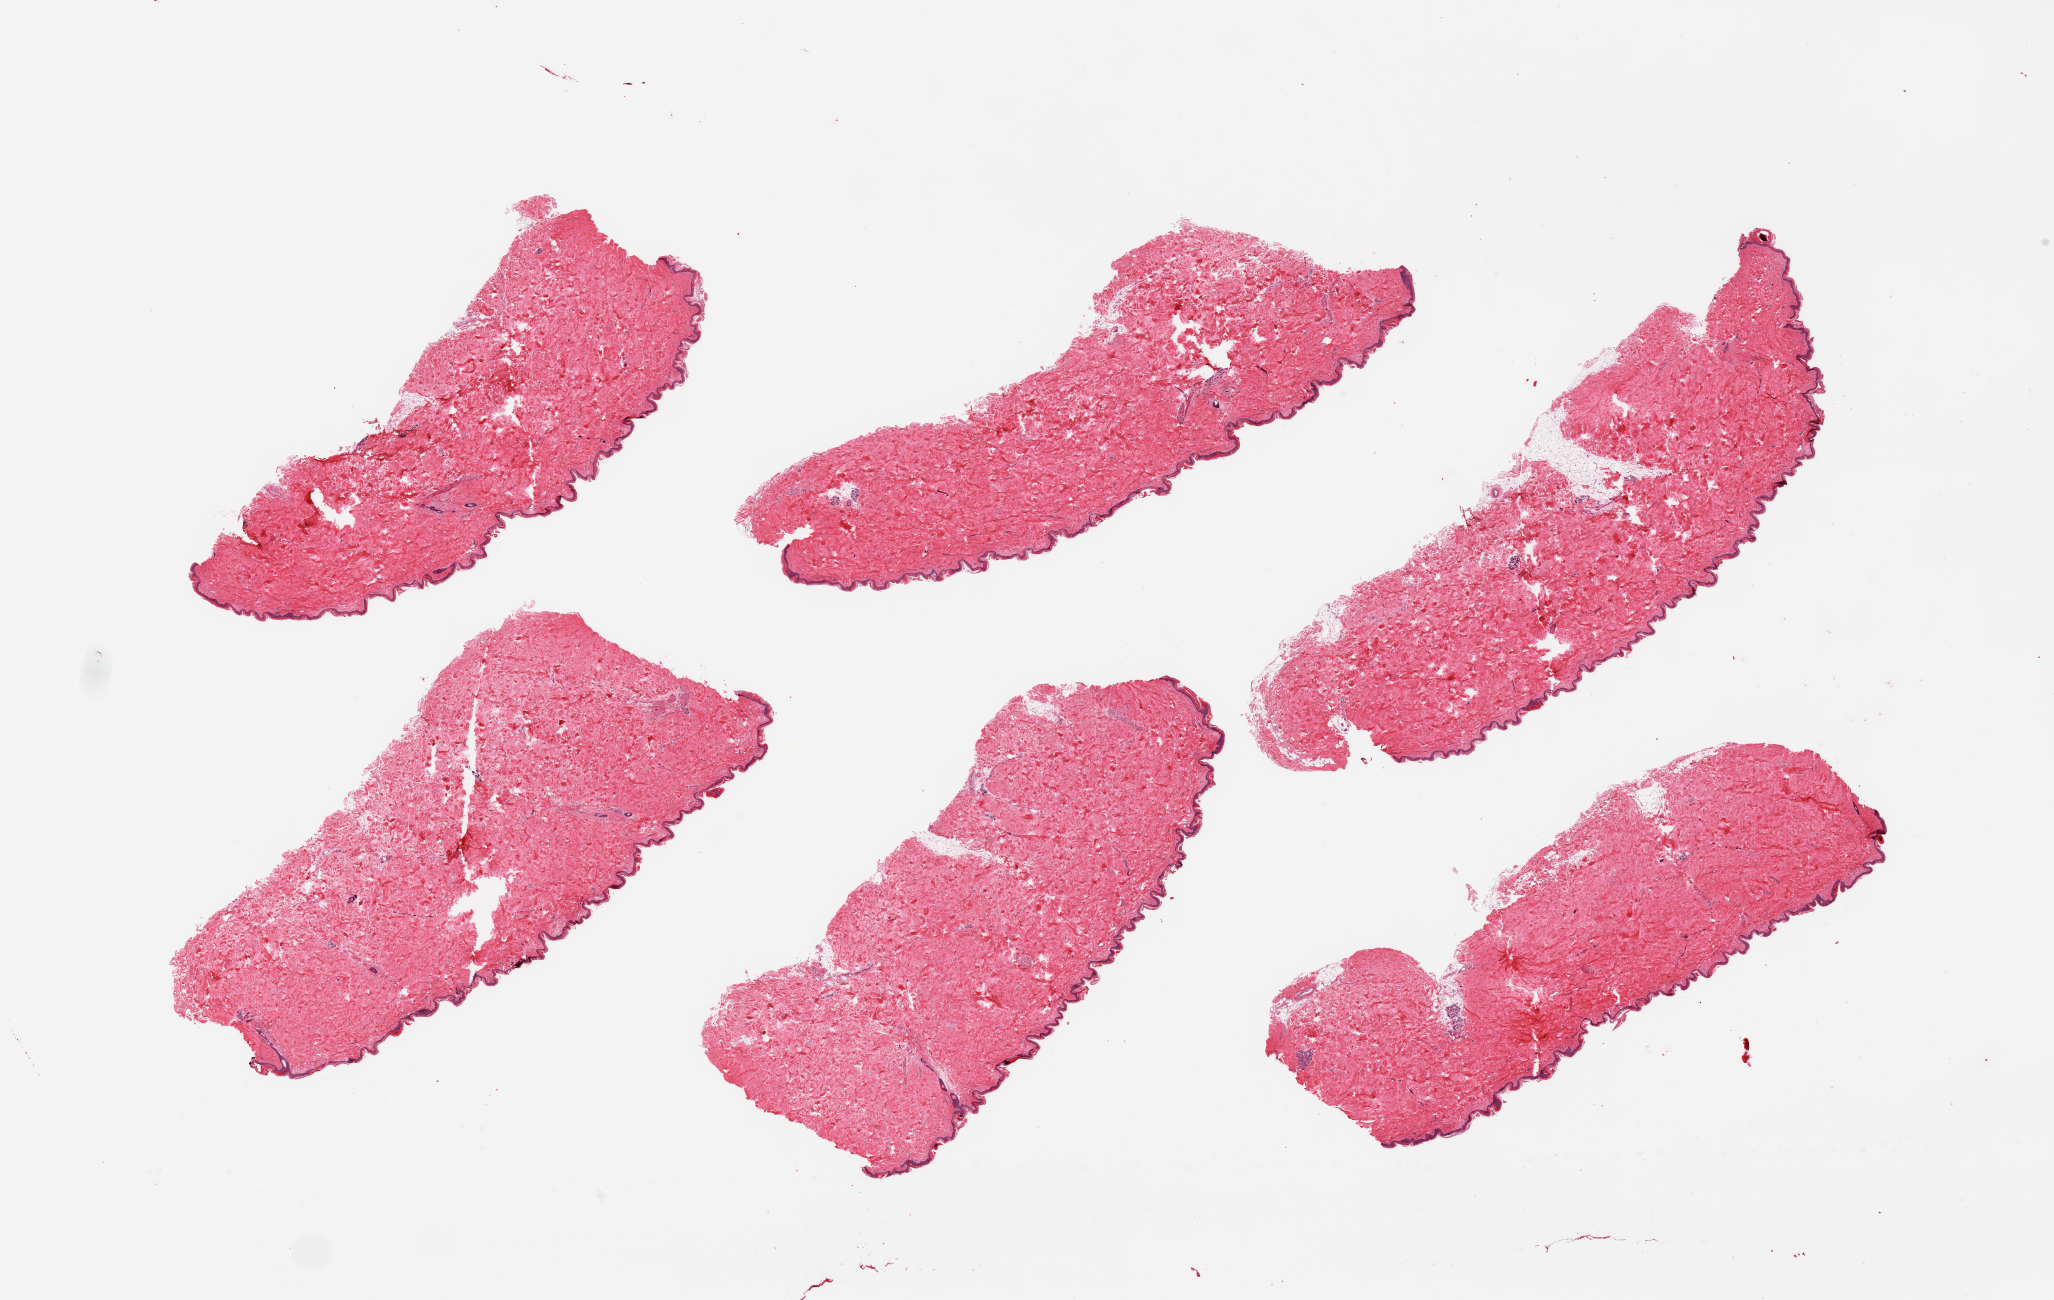
Digitized H&E-stained section — a low-resolution overview of the entire scanned area, about 32.5 x 20.6 mm (from a 20x scan), PAXgene-fixed paraffin-embedded (PFPE) section, sampled site (target tissue): skin of suprapubic region, donor tissue sample.
Review note (as recorded): 6 pieces.